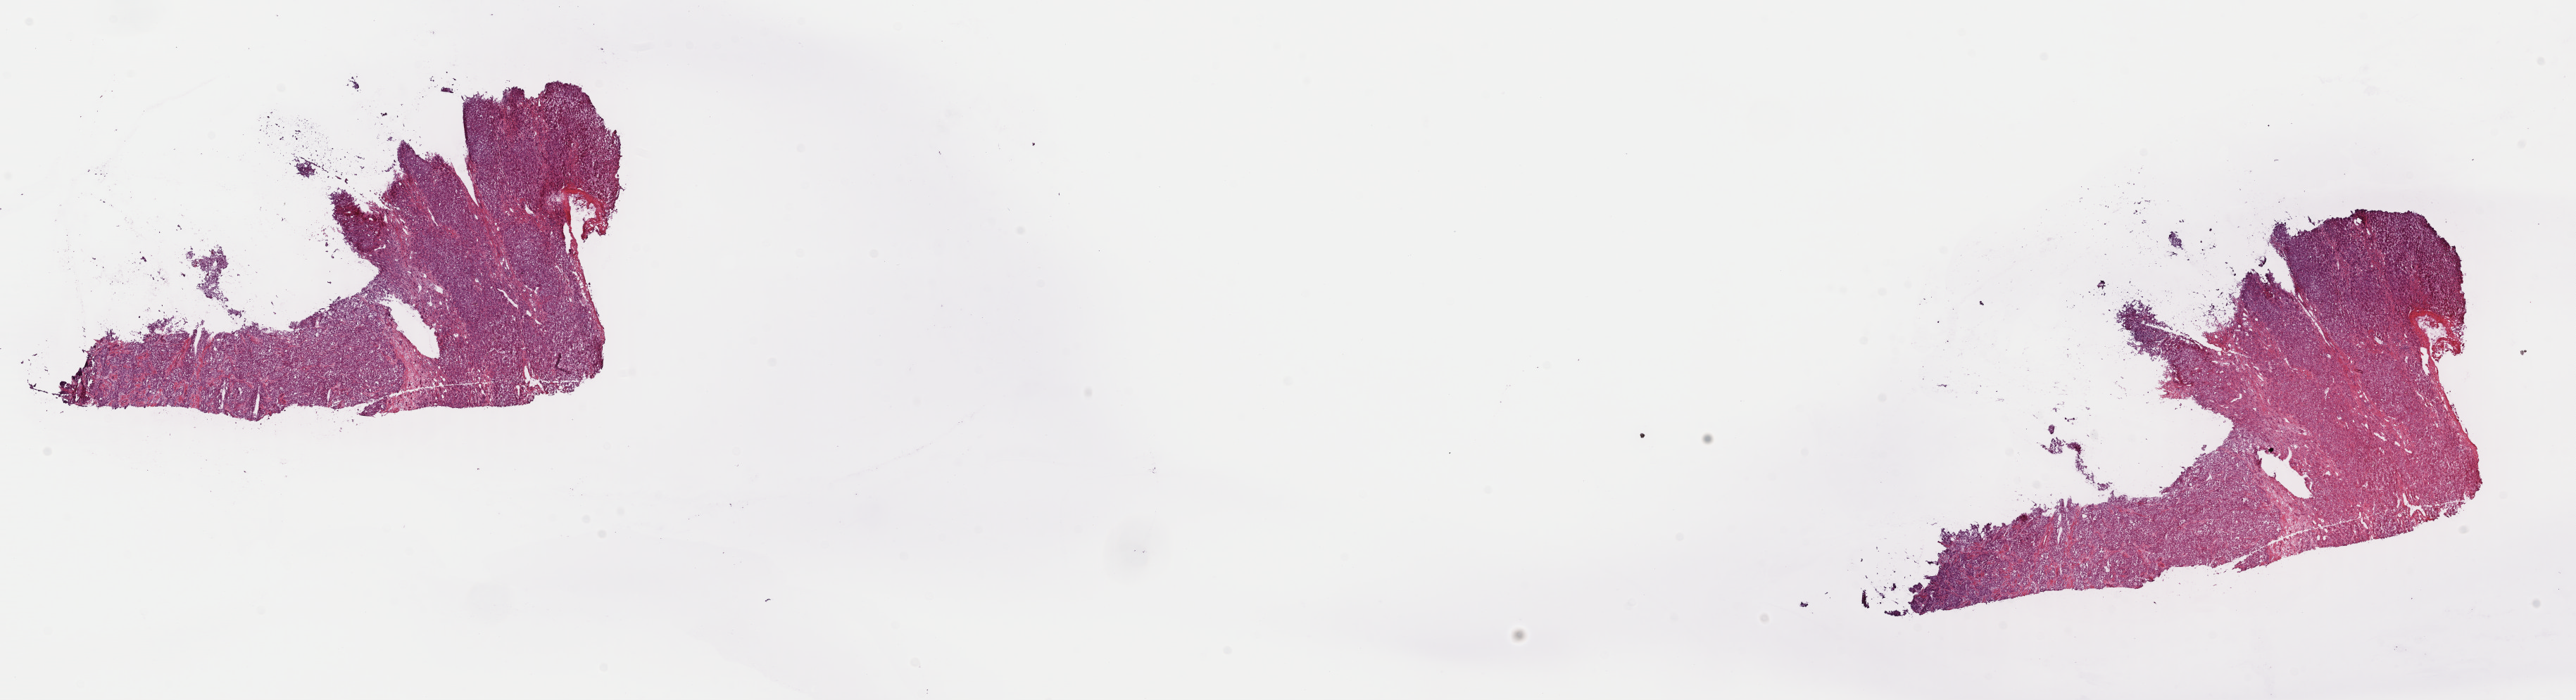
Digitized Hematoxylin and eosin (H&E) stained tissue section (whole slide) — low-resolution overview of the scanned area, about 28.9 x 7.8 mm (from a 40x scan). Frozen section from the top of the tissue portion. Primary tumour sample from the liver. Patient: male, age at initial diagnosis 58 years. Pathologist review of this section (percent, as recorded): tumour cells 80%, tumour nuclei 75%.
Histologic diagnosis: Hepatocellular carcinoma, NOS.